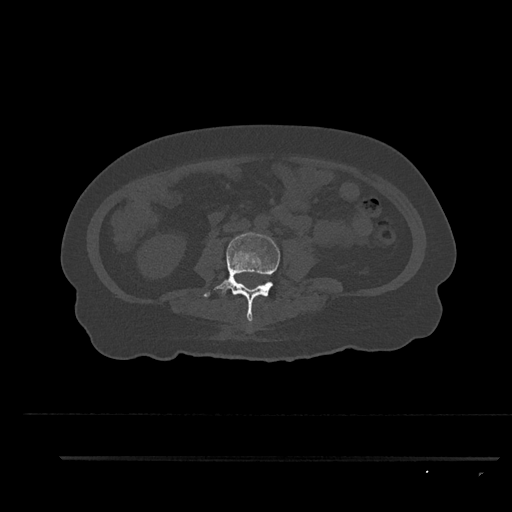
CT including the spine, one axial slice; position 82 of 797 along the scan axis; bone window (W 1800 / L 400 HU); 0.5 mm slice thickness; 512 × 512 image matrix, field of view 408 × 408 mm. Patient: female, 44 years. From the clinical record (not read from this slice): primary cancer: renal; vertebrae with lytic lesions (as recorded): L1.
Annotated regions visible in this slice (semi-automatic segmentation, software-assisted and operator-edited):
- L3 vertebra: bounding box <203,232,280,322> (left, top, right, bottom; pixels)